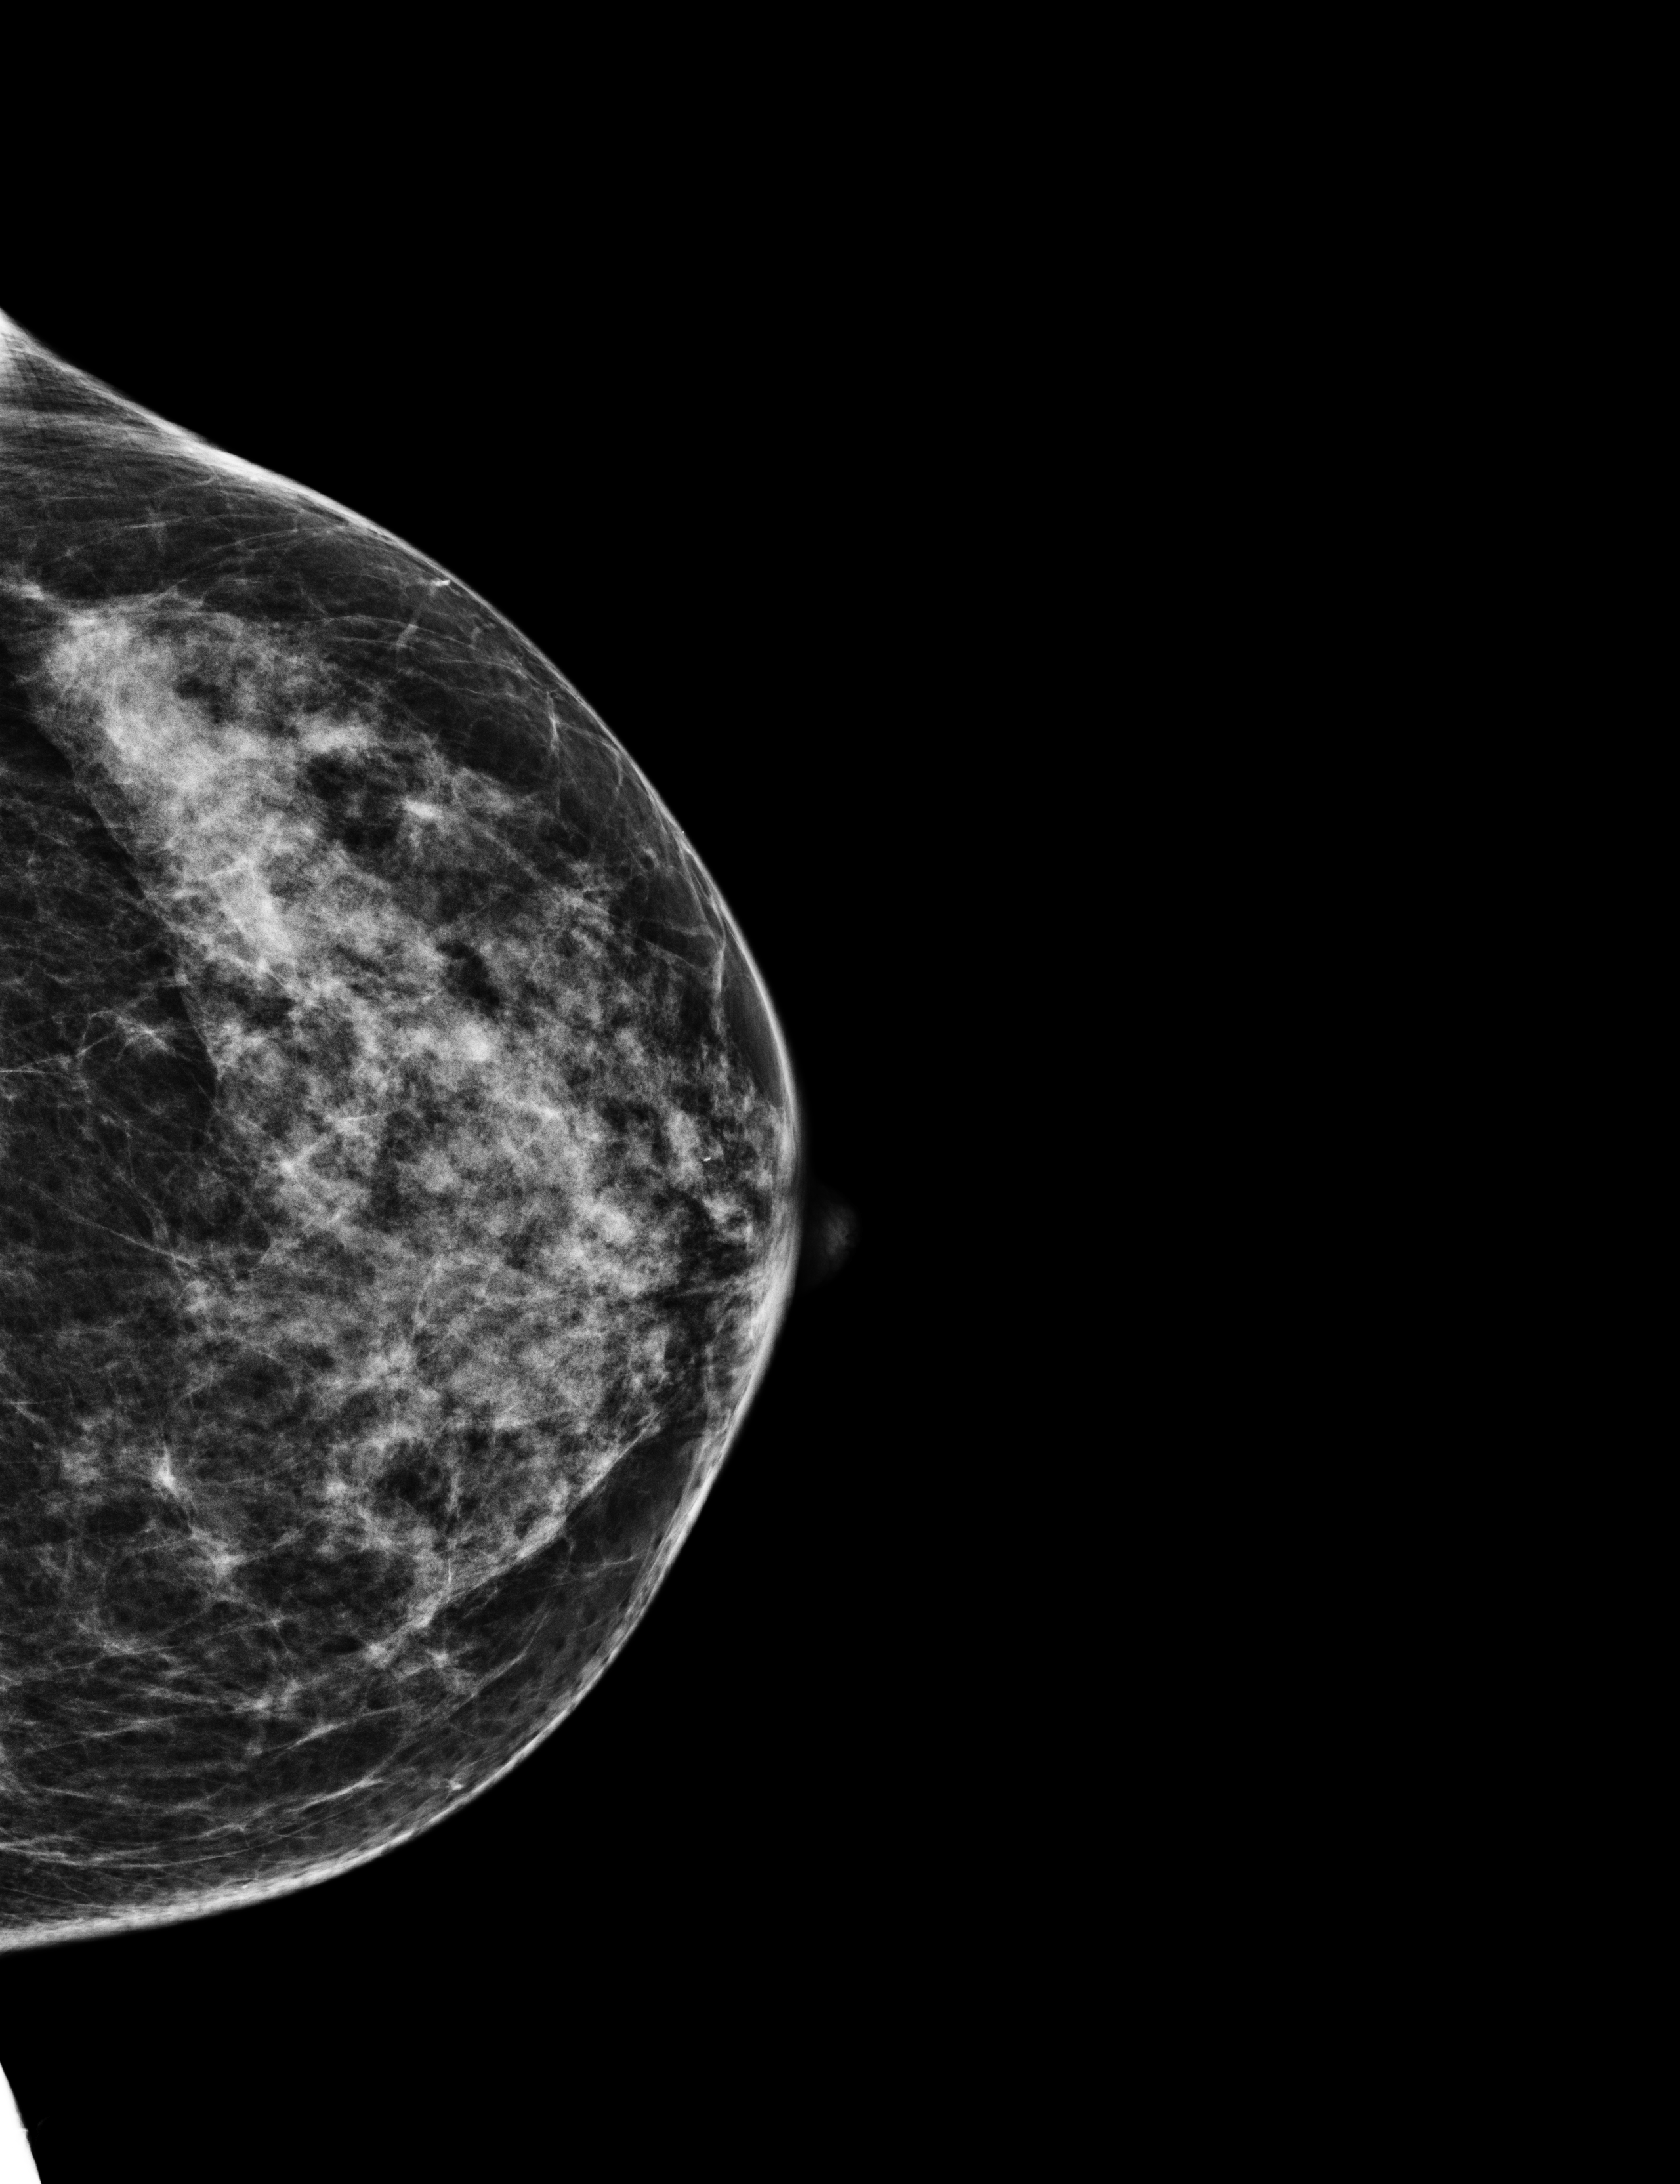
Annual screening mammography examination. Patient: female, 61 years.
Image type: full-field digital mammogram. Breast: left. Projection: cranio-caudal projection. BI-RADS breast density category at the screening exam (both breasts, scale 1–4): 3. Final BI-RADS category for the screening round (tomosynthesis exam, both breasts): category 1. Recall: no recall after this screen.